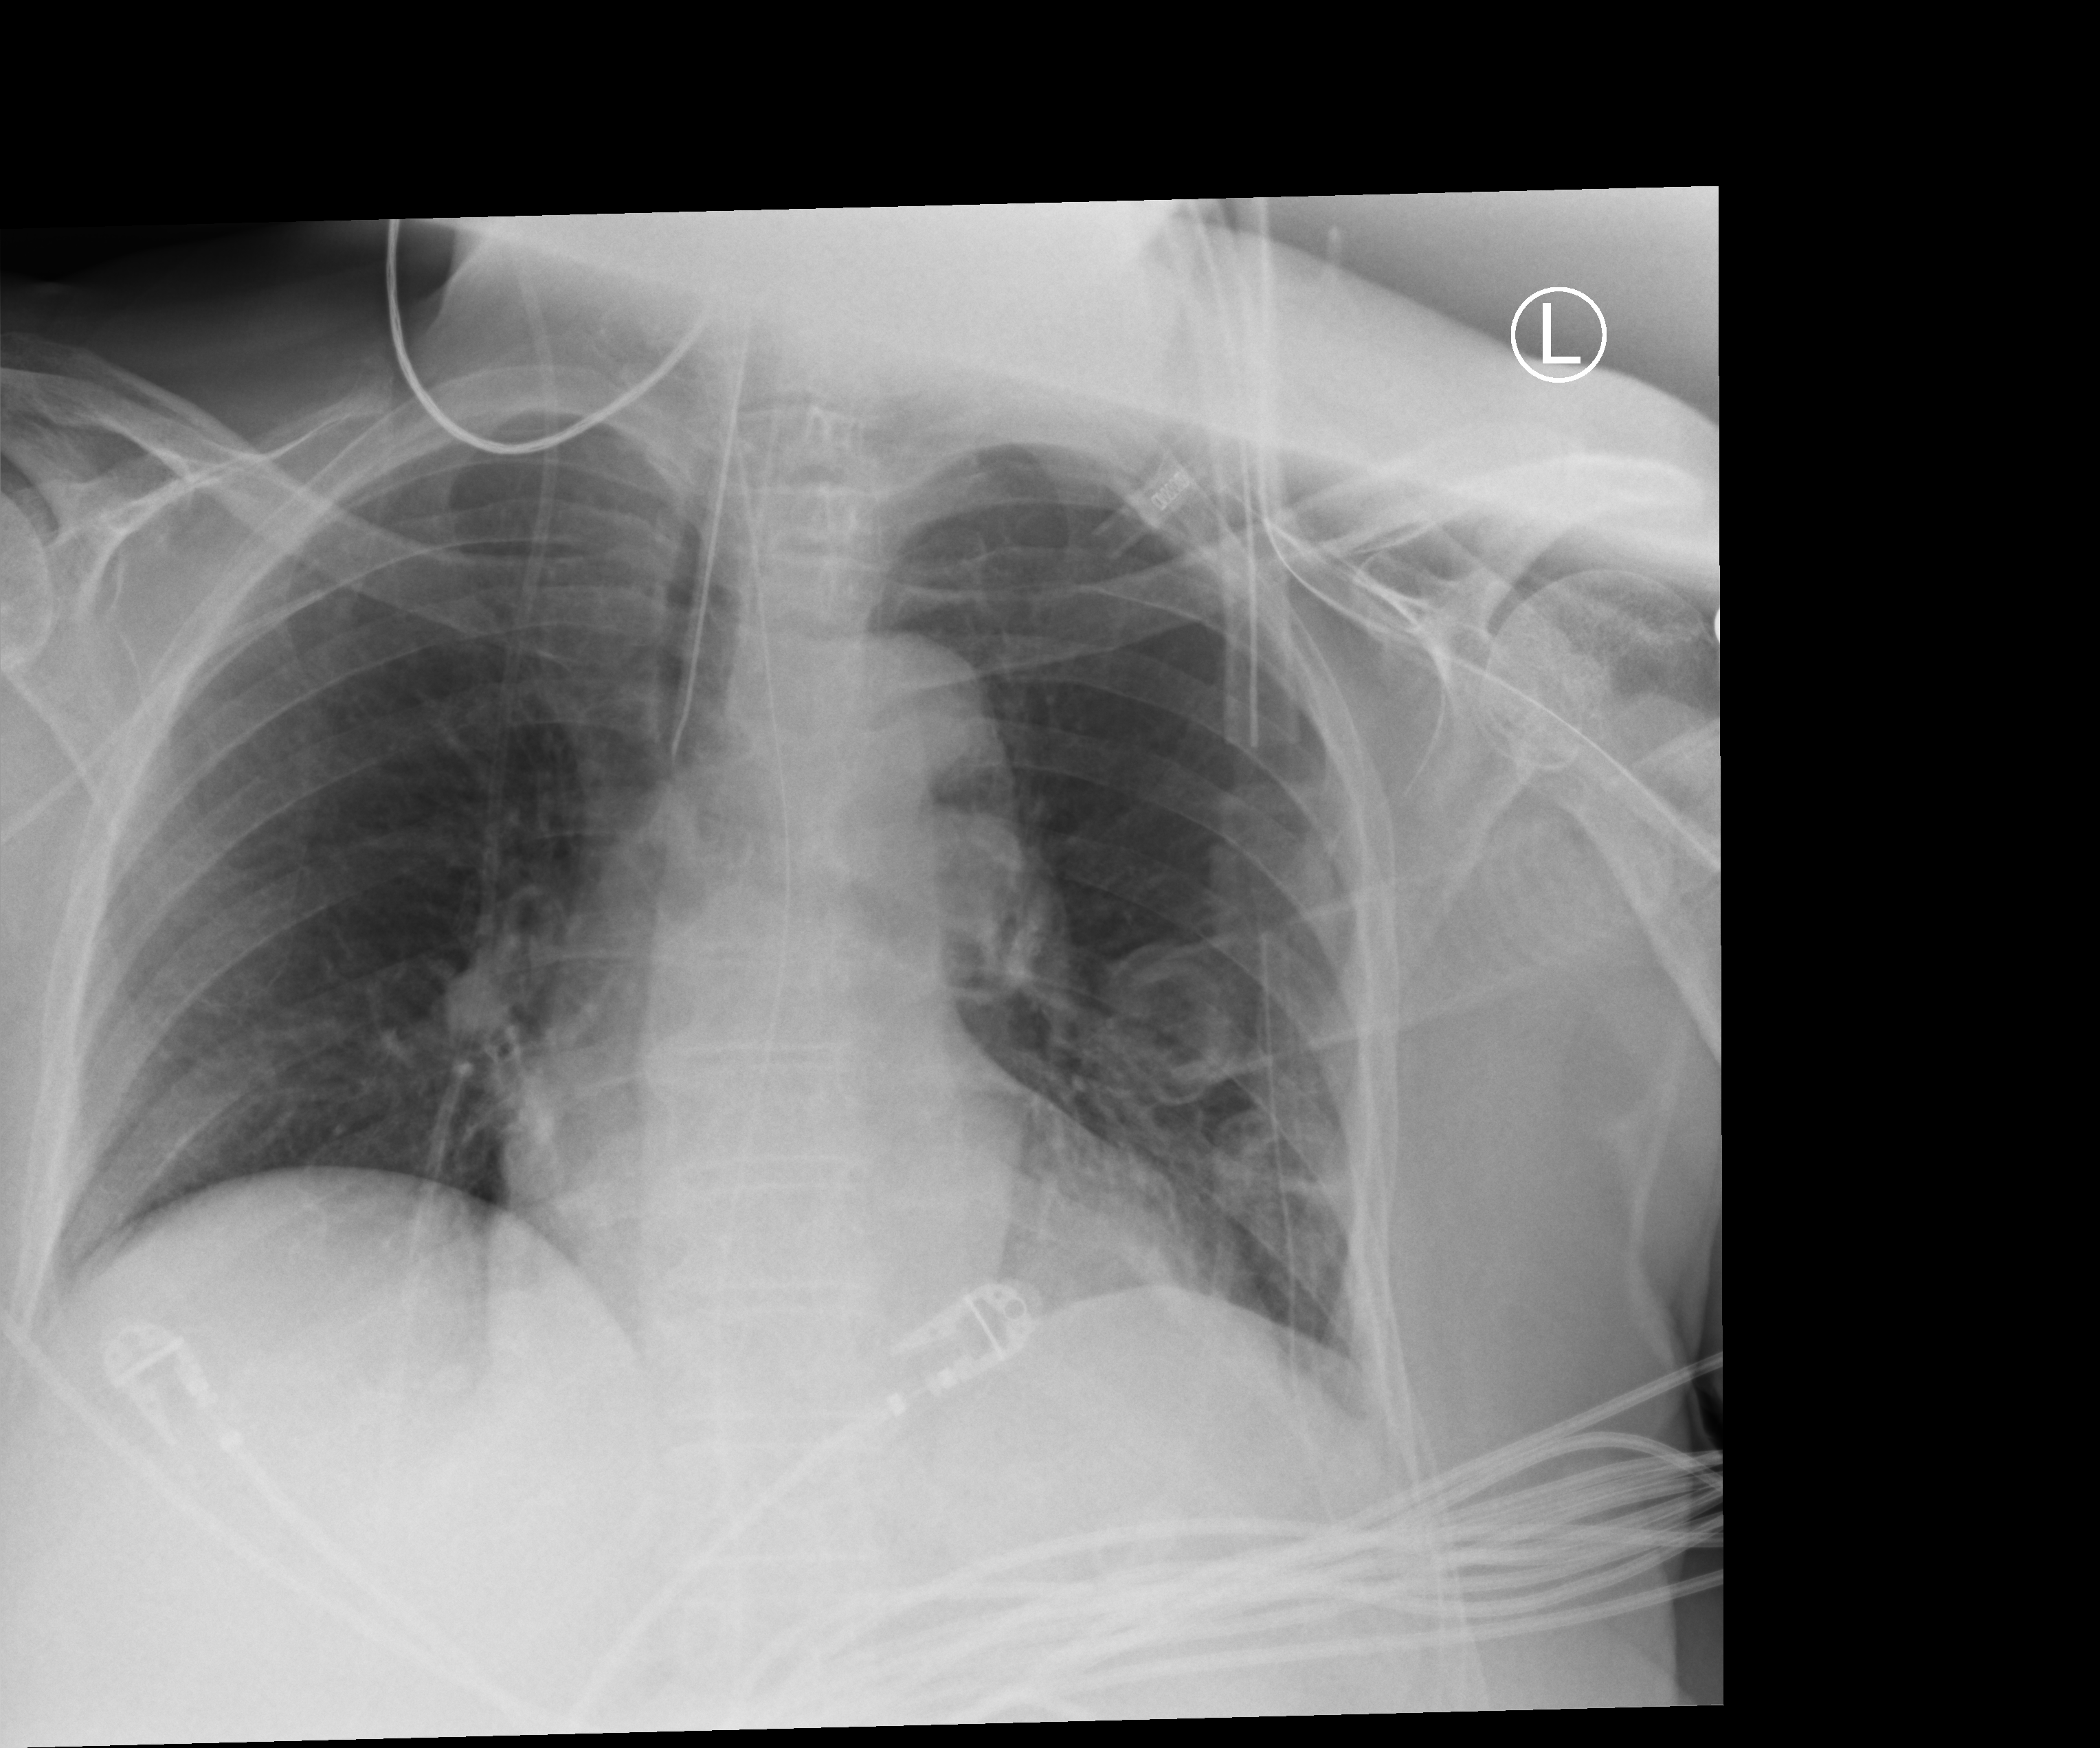
Portable chest radiograph; anteroposterior (AP) projection. Female patient hospitalised with COVID-19, age 75–90 years.
Hospital-stay facts (about this admission, not read from this image; timing relative to this image not recorded): mechanically ventilated during this hospital stay: yes.